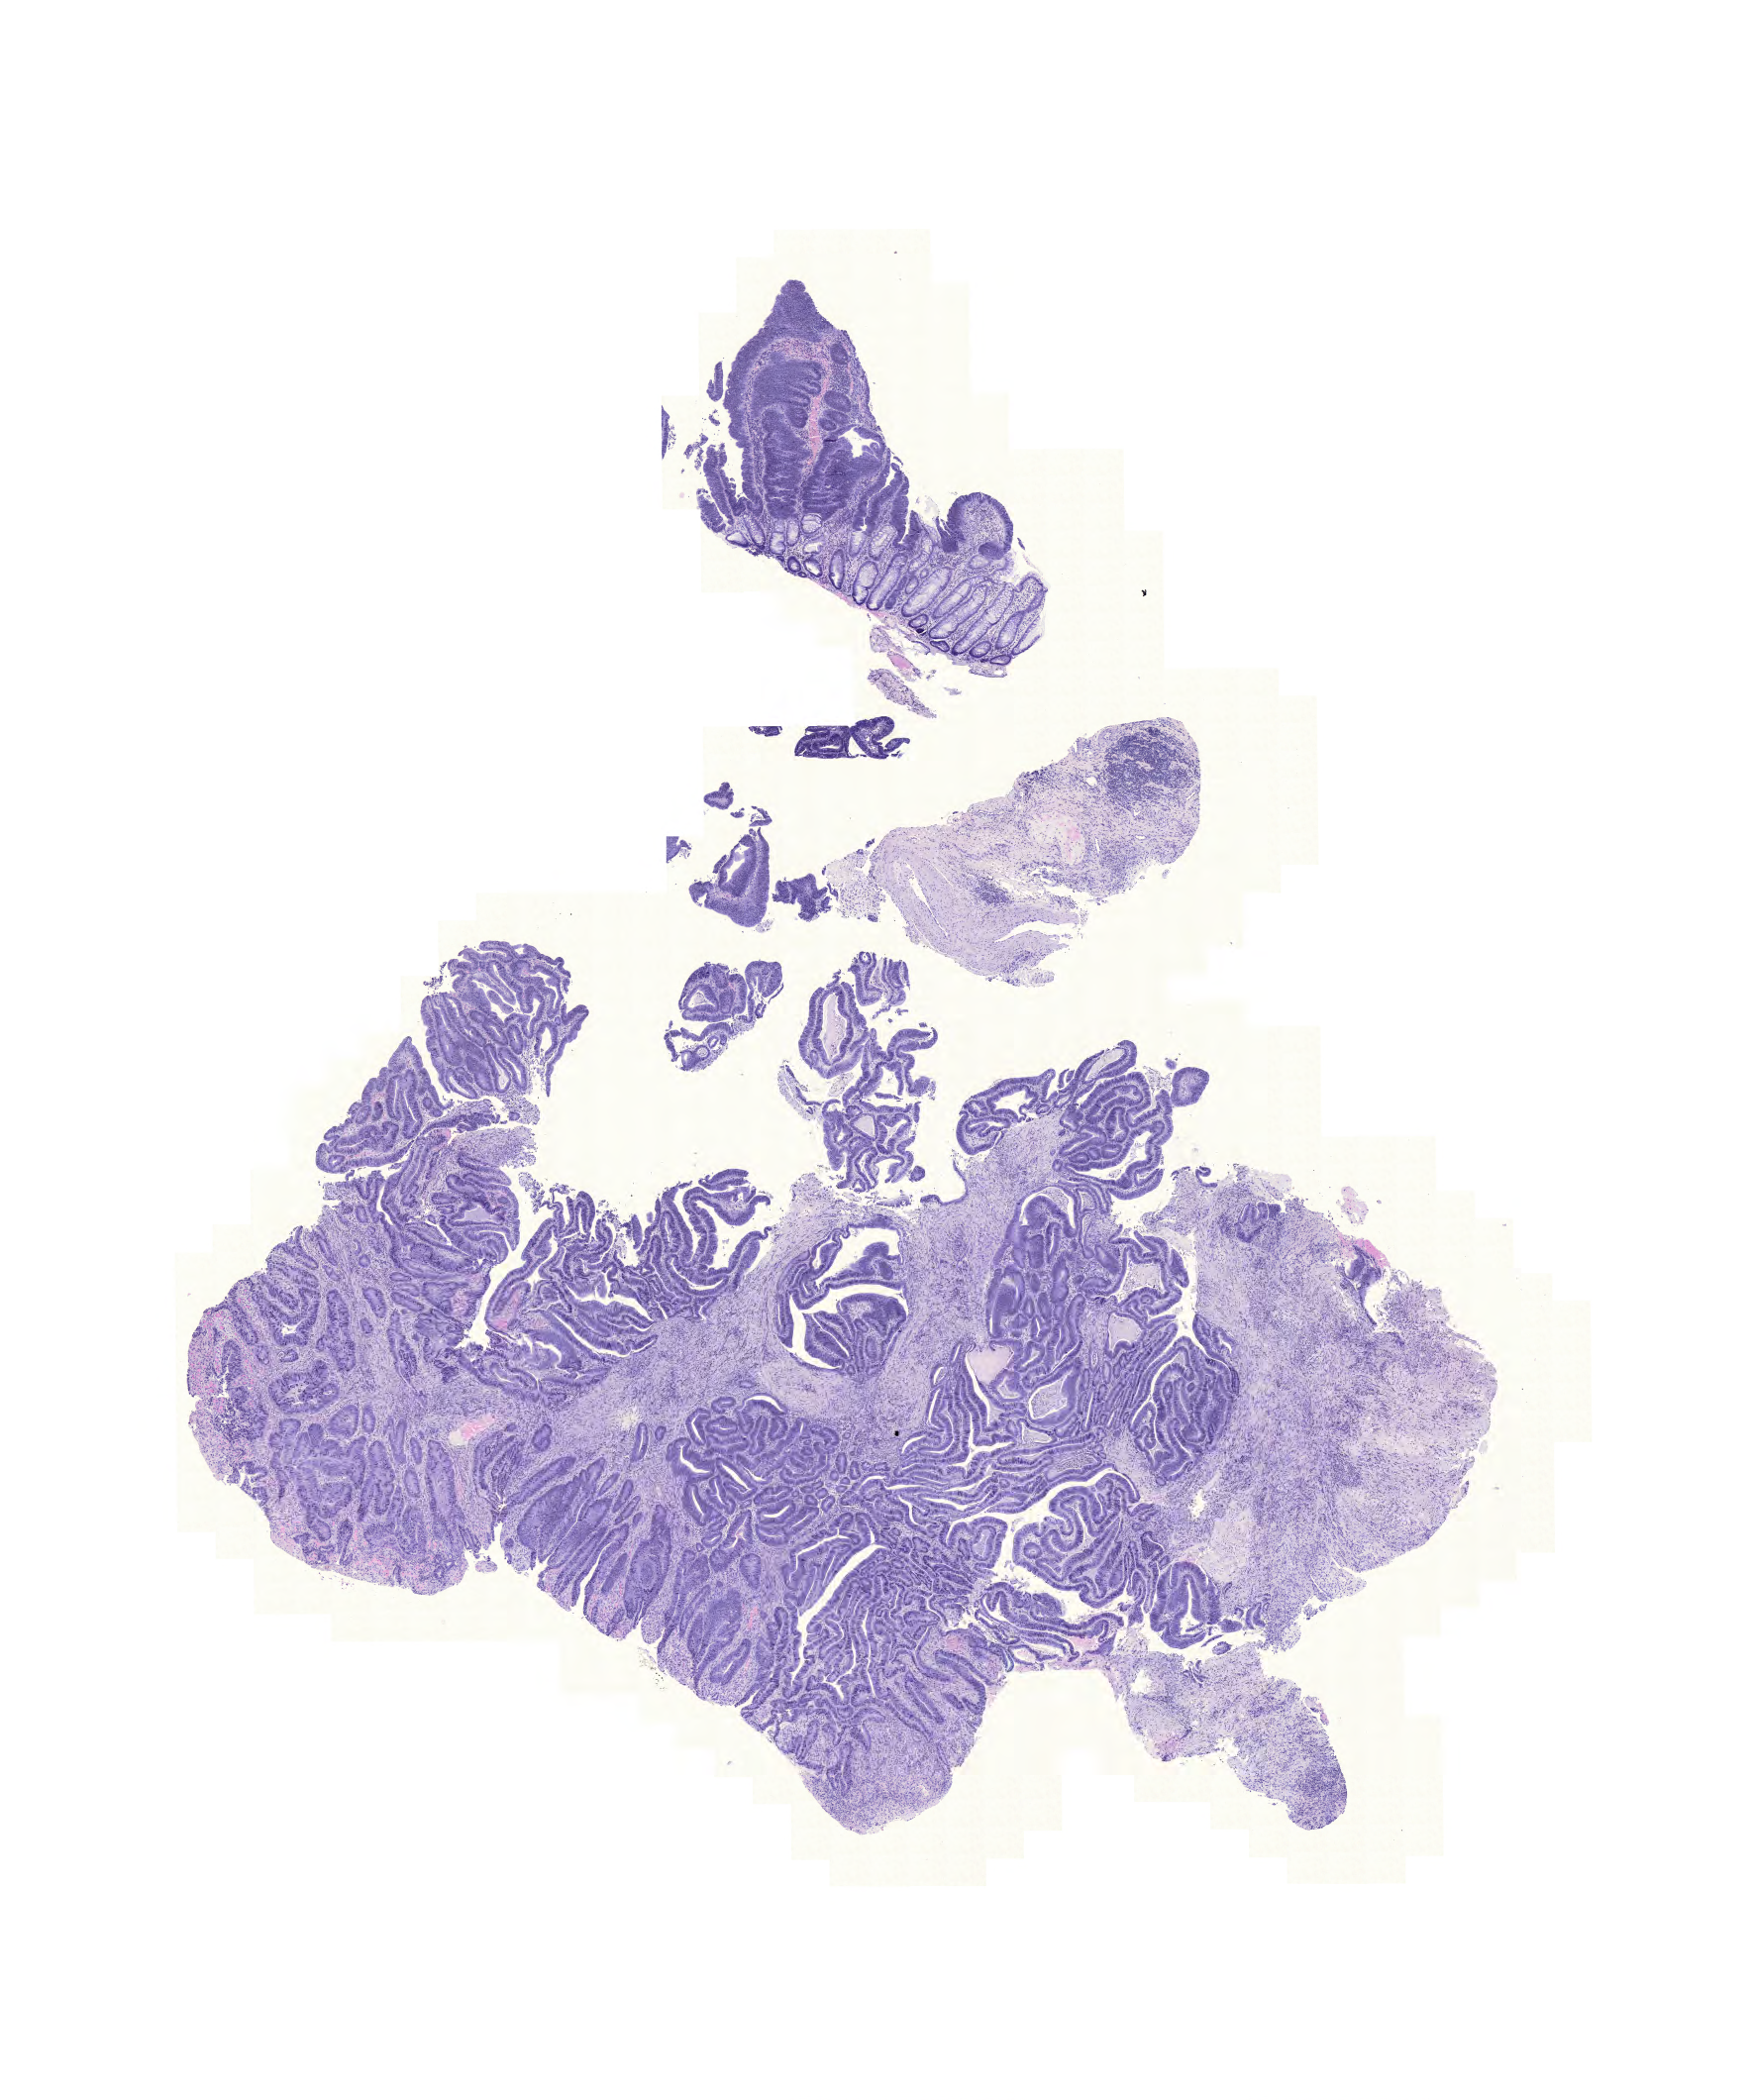
H&E-stained whole-slide image — whole scanned area (about 13.2 x 15.8 mm) shown as a low-resolution overview; FFPE section; colon, primary tumour sample. Male, age 72 years at initial diagnosis.
- AJCC pathologic stage: I (6th edition)
- histologic diagnosis: Adenocarcinoma, NOS